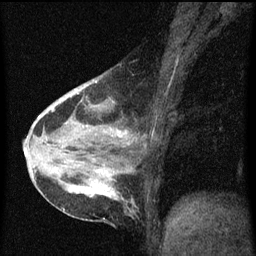
Breast MRI (dynamic contrast-enhanced), one sagittal slice. Dynamic contrast-enhanced series, image 2 of 3 at this slice position (ordered by acquisition). 1.5 T. TE 4.2 ms, TR 8 ms. 2 mm slice thickness. 256 × 256 image matrix. Female patient, age 38 years.
Annotated regions visible in this slice (semi-automatically segmented with operator editing):
- analysis volume of interest (the breast-tissue region the enhancement analysis was run in; not a lesion): bounding box (x1, y1, x2, y2) in pixels: (61, 76, 141, 147)
- tumour enhancement mask (voxels above the 70 % enhancement threshold inside the analysis volume of interest): (70, 80, 130, 145)